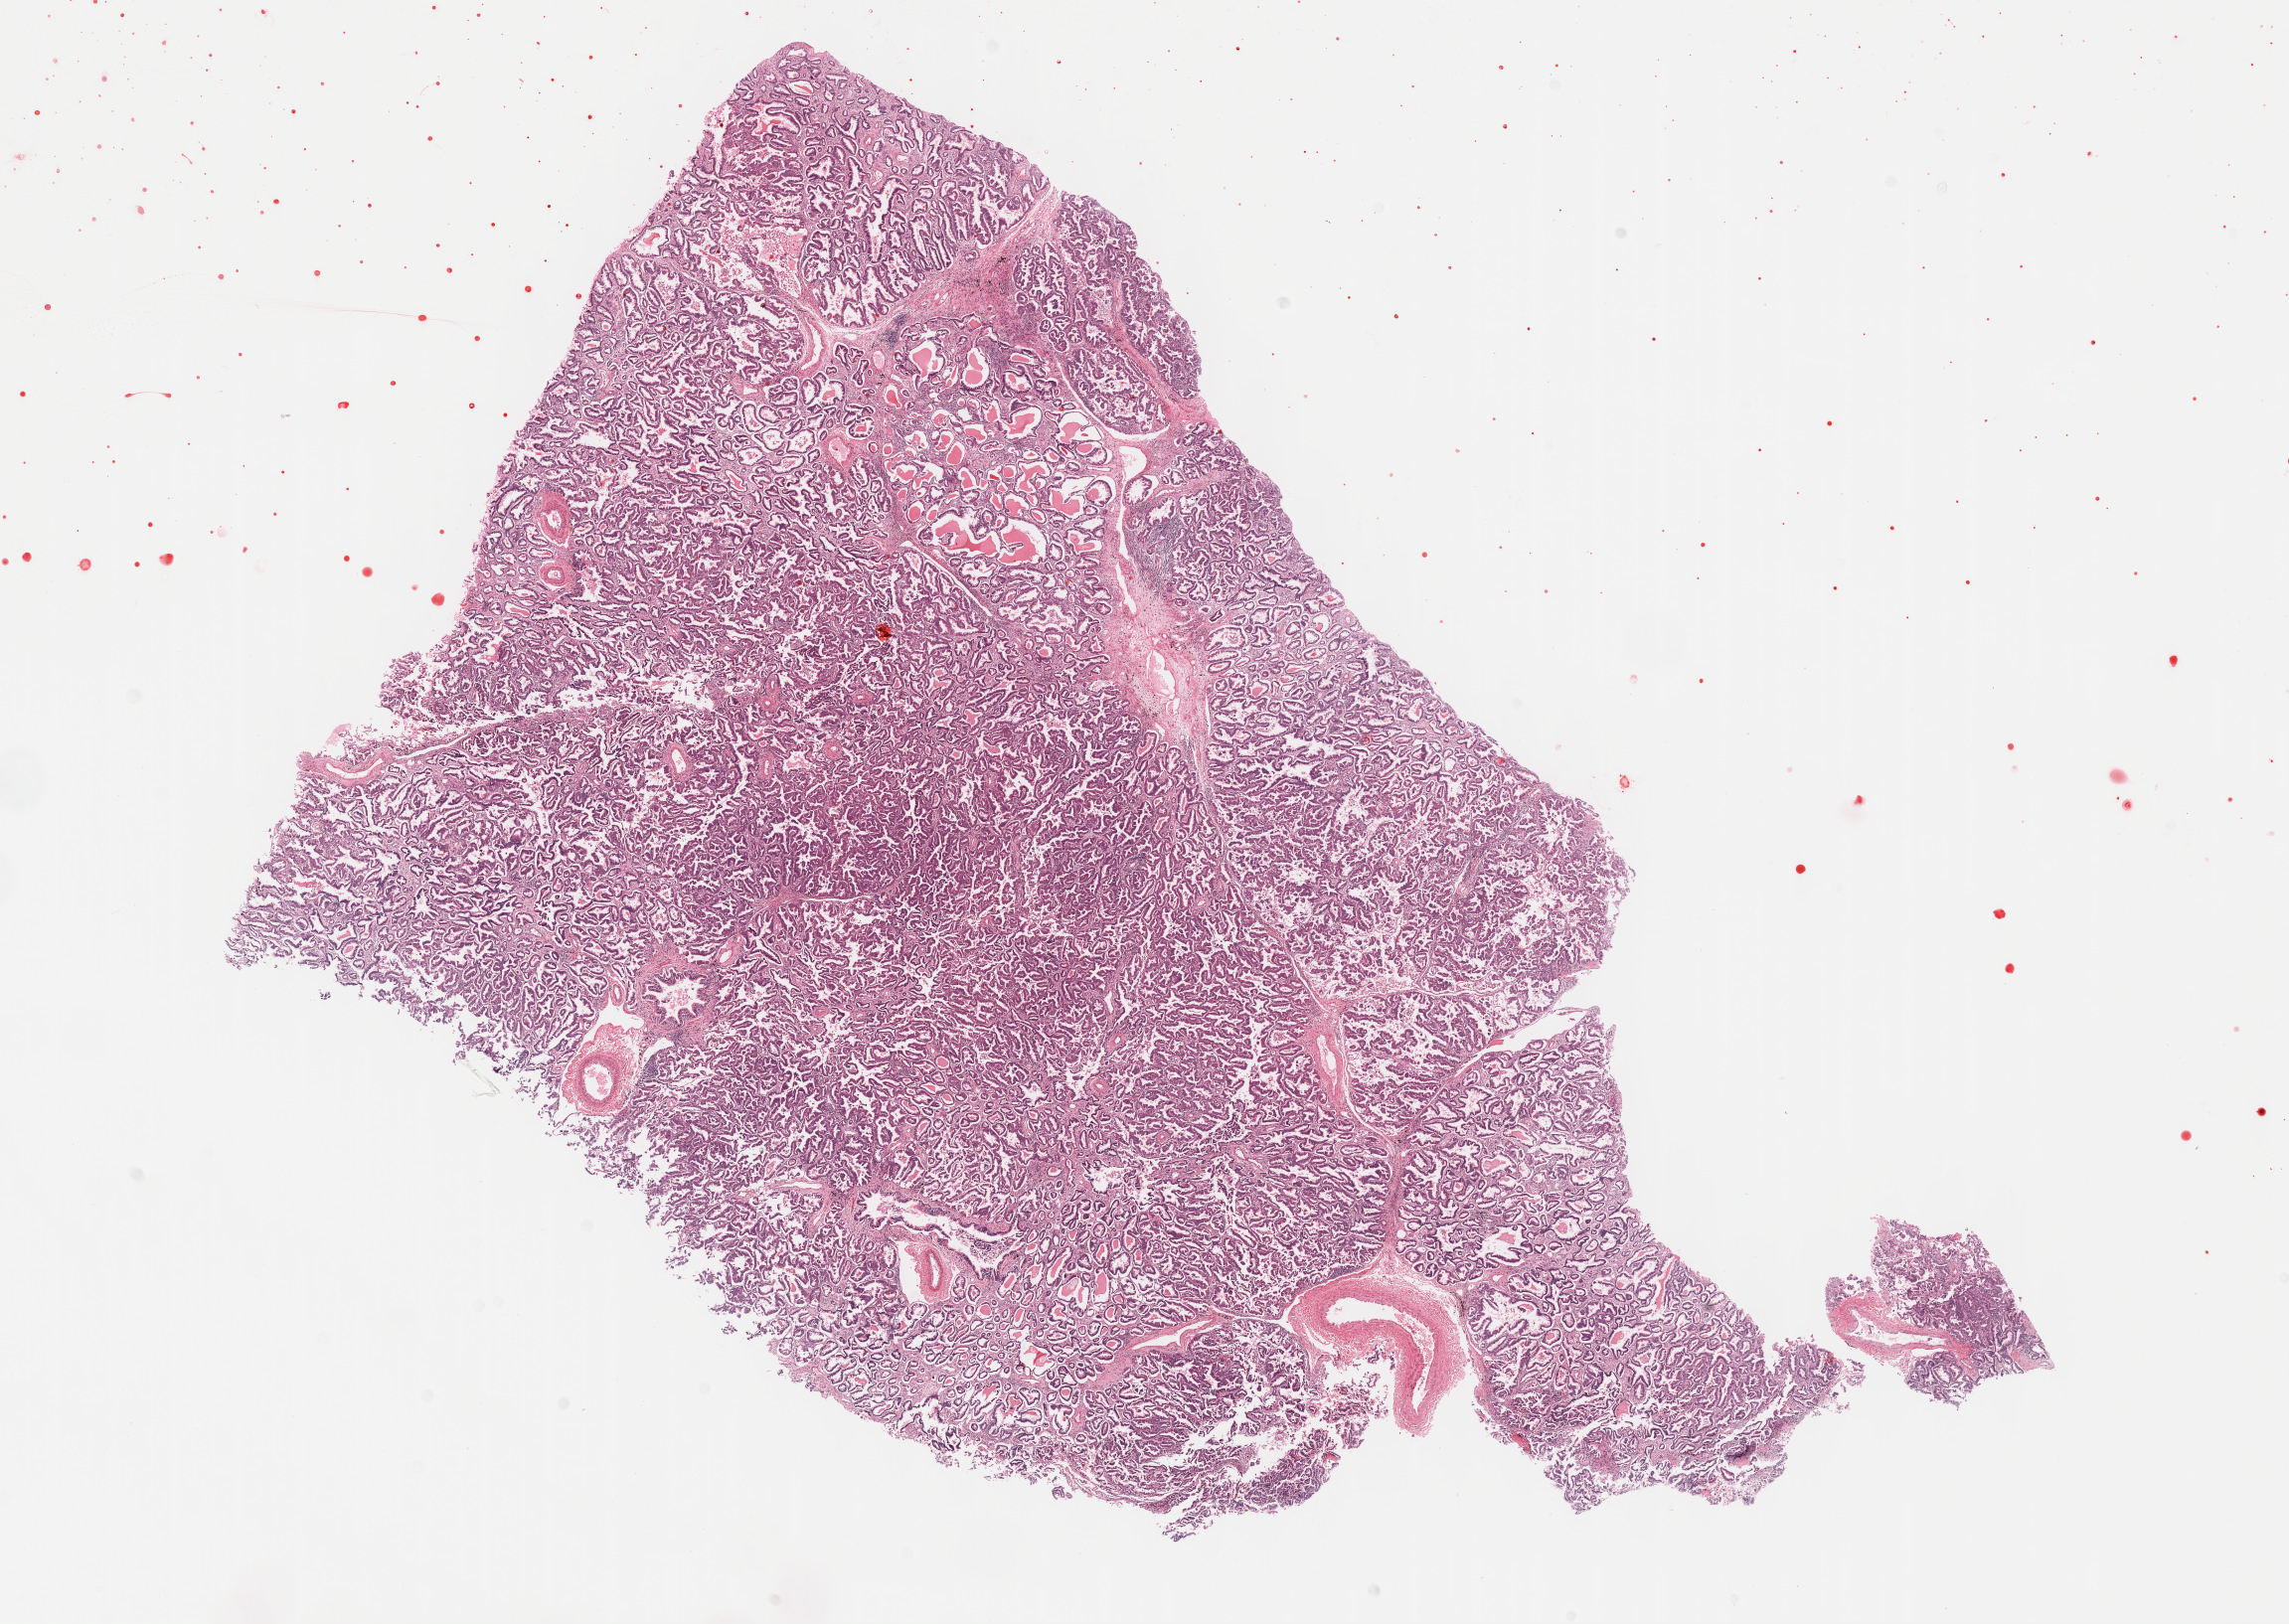
Whole-slide histology image, H&E-stained, a low-resolution overview of the entire scanned area, about 18.6 x 13.2 mm. FFPE section. Lung, primary tumour sample. Patient: male, age at initial diagnosis 63 years.
Laterality: right. Pathologic diagnosis: Adenocarcinoma with mixed subtypes (overlapping lesion of lung). AJCC pathologic stage: IV (6th edition).